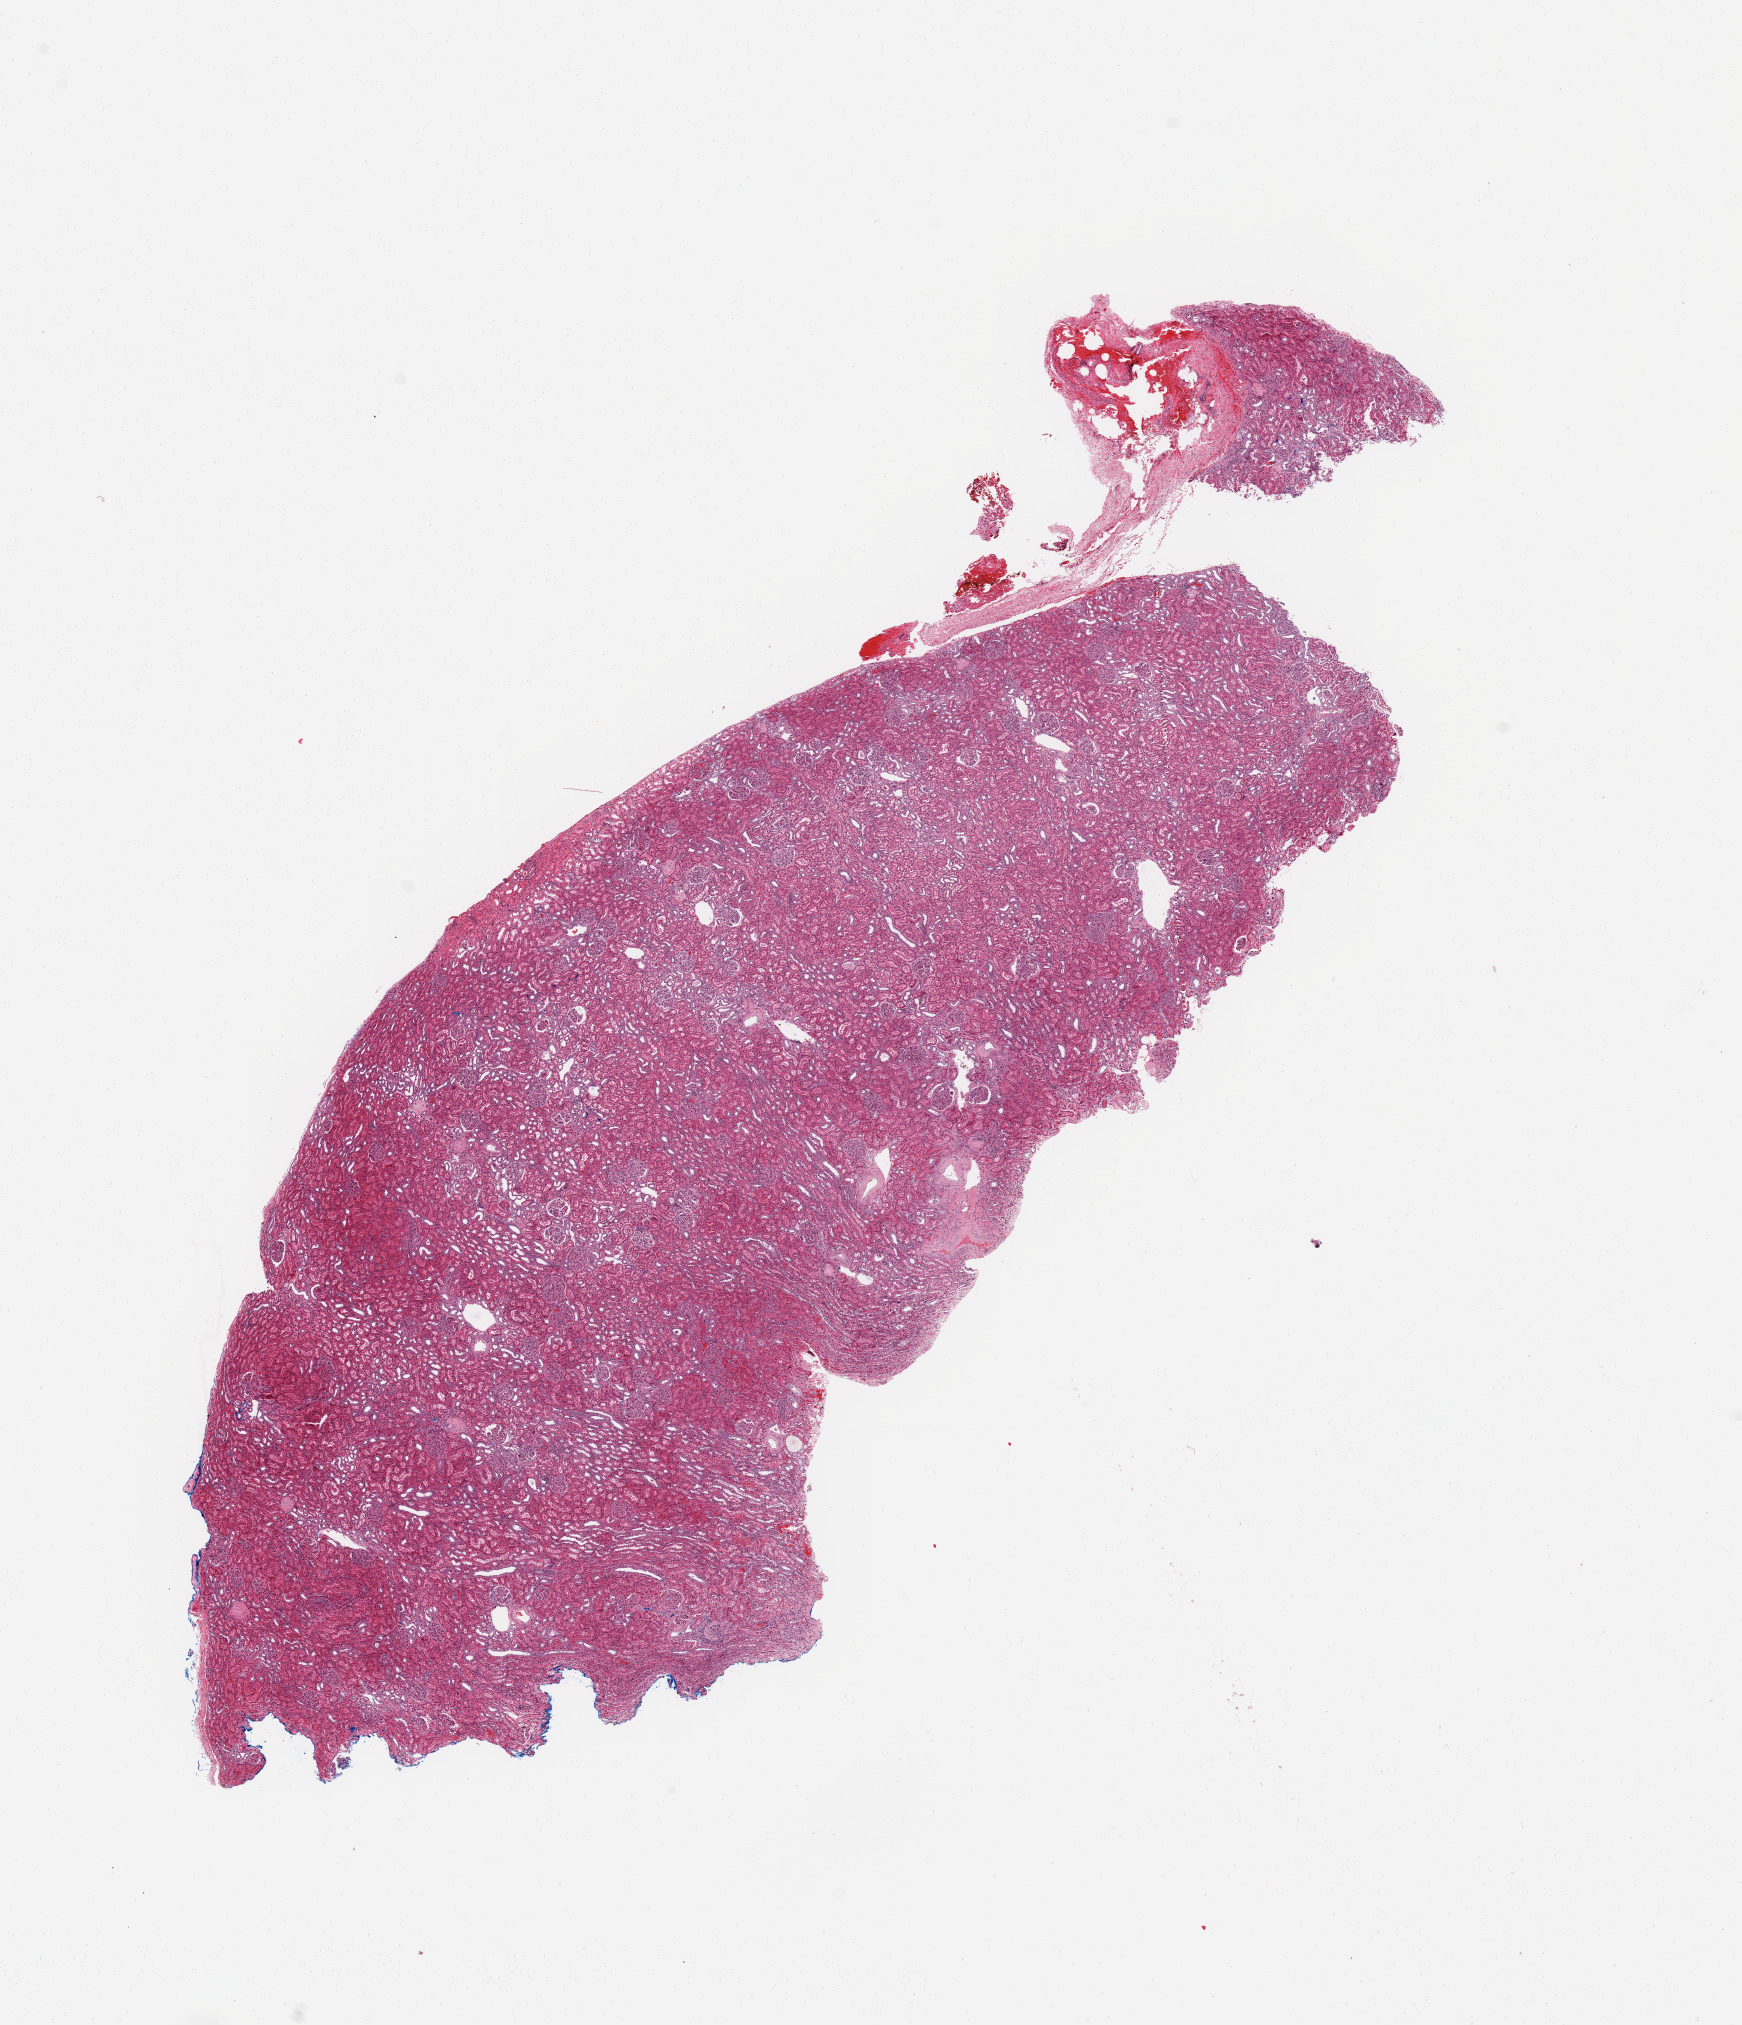
Whole-slide histology image, H&E-stained — shown as a low-resolution overview of the whole scanned area (about 13.8 x 16.0 mm); normal (non-tumour) tissue sample, sampled site: kidney. Female, 65 y/o.
This section: normal (non-tumour) tissue from the same patient. Patient diagnosis: Renal cell carcinoma, NOS.